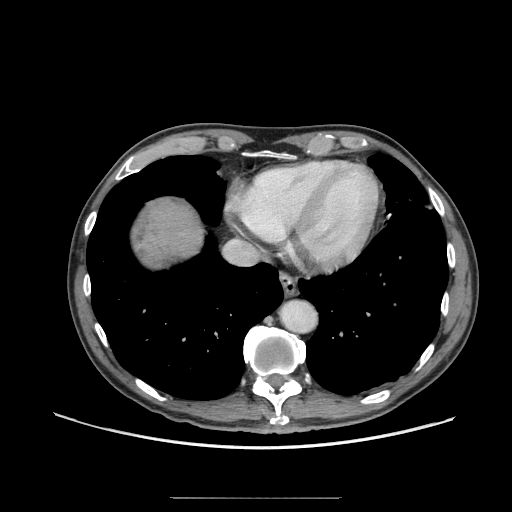
Contrast-enhanced abdominal CT (liver protocol), one axial slice; position 65 of 71 along the scan axis; reconstruction kernel STANDARD; soft-tissue window (W 400 / L 40 HU); 2.5 mm slice thickness; 512 × 512 image matrix, field of view 400 × 400 mm. Case-level facts recorded for this patient, not image findings: diagnosis: hepatocellular carcinoma (patient treated with transarterial chemoembolisation; whether this scan precedes or follows treatment is not stated here); TNM stage (as recorded): Stage-I.
Structures marked on this image (semi-automatic segmentation, software-assisted and operator-edited):
- abdominal aorta: bounding box (x1, y1, x2, y2) in pixels: (281, 301, 316, 332)
- liver parenchyma outside the tumour (the mass and vessels are separate outlines, so this box may not span the whole liver): (139, 202, 202, 262)